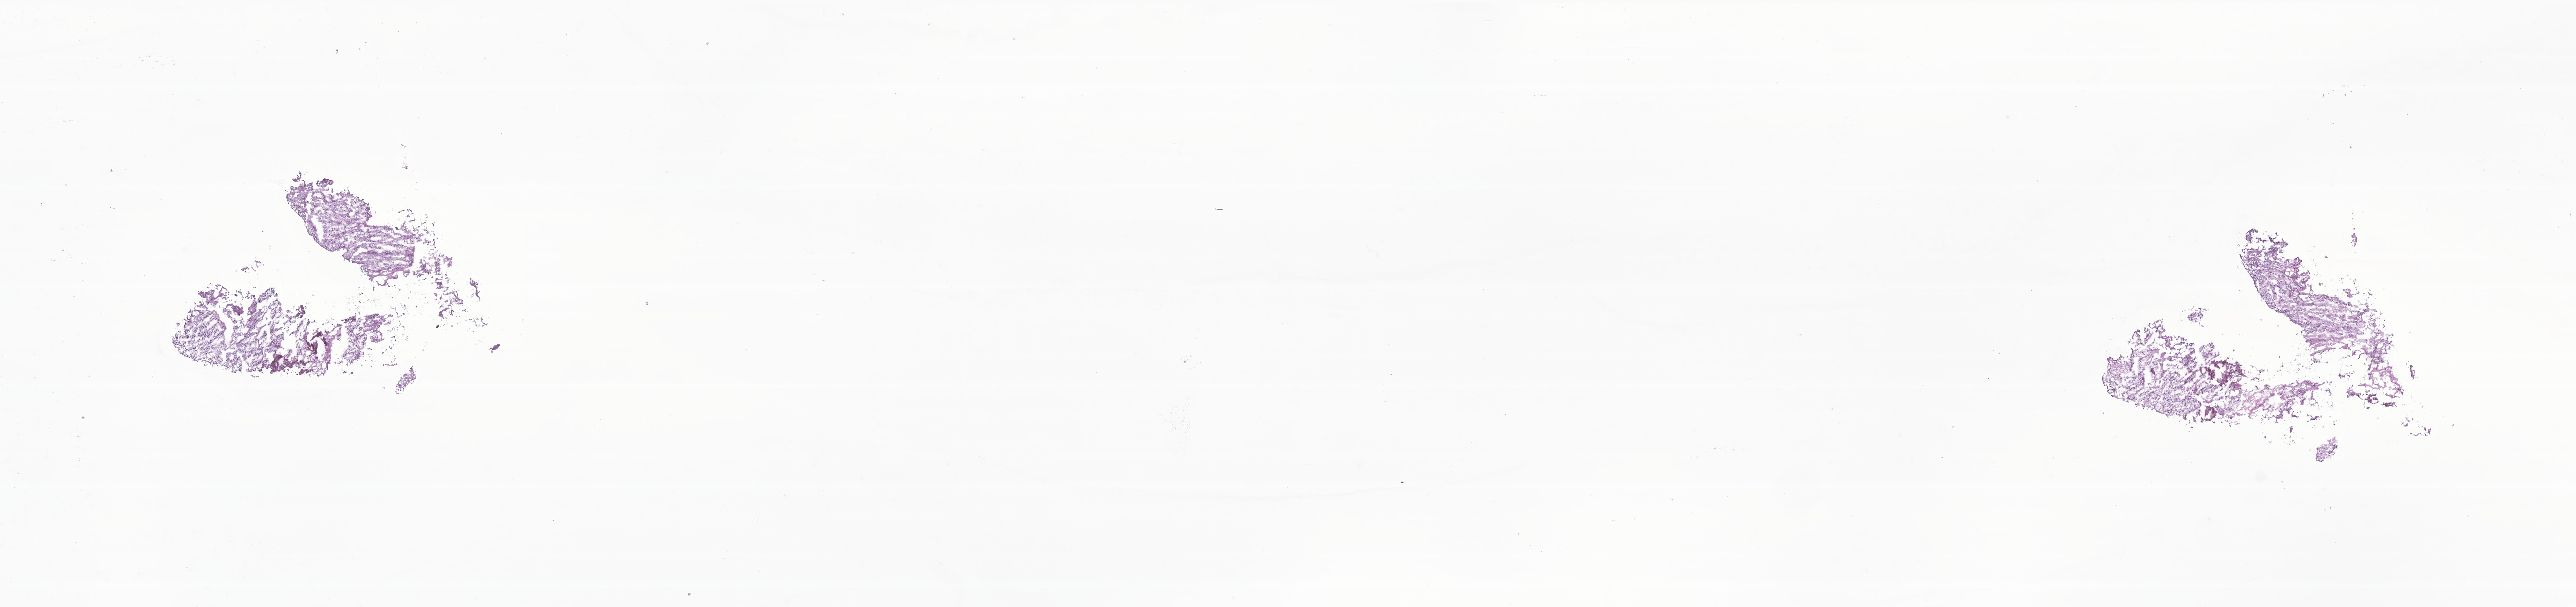
Whole-slide image, hematoxylin and eosin (H&E) stain of tumor tissue from the kidney, whole scanned area (about 27.6 x 6.5 mm) shown as a low-resolution overview; frozen section. Patient female; age 582 days (about 1.6 years).
Recorded diagnosis: Neuroblastoma, NOS.